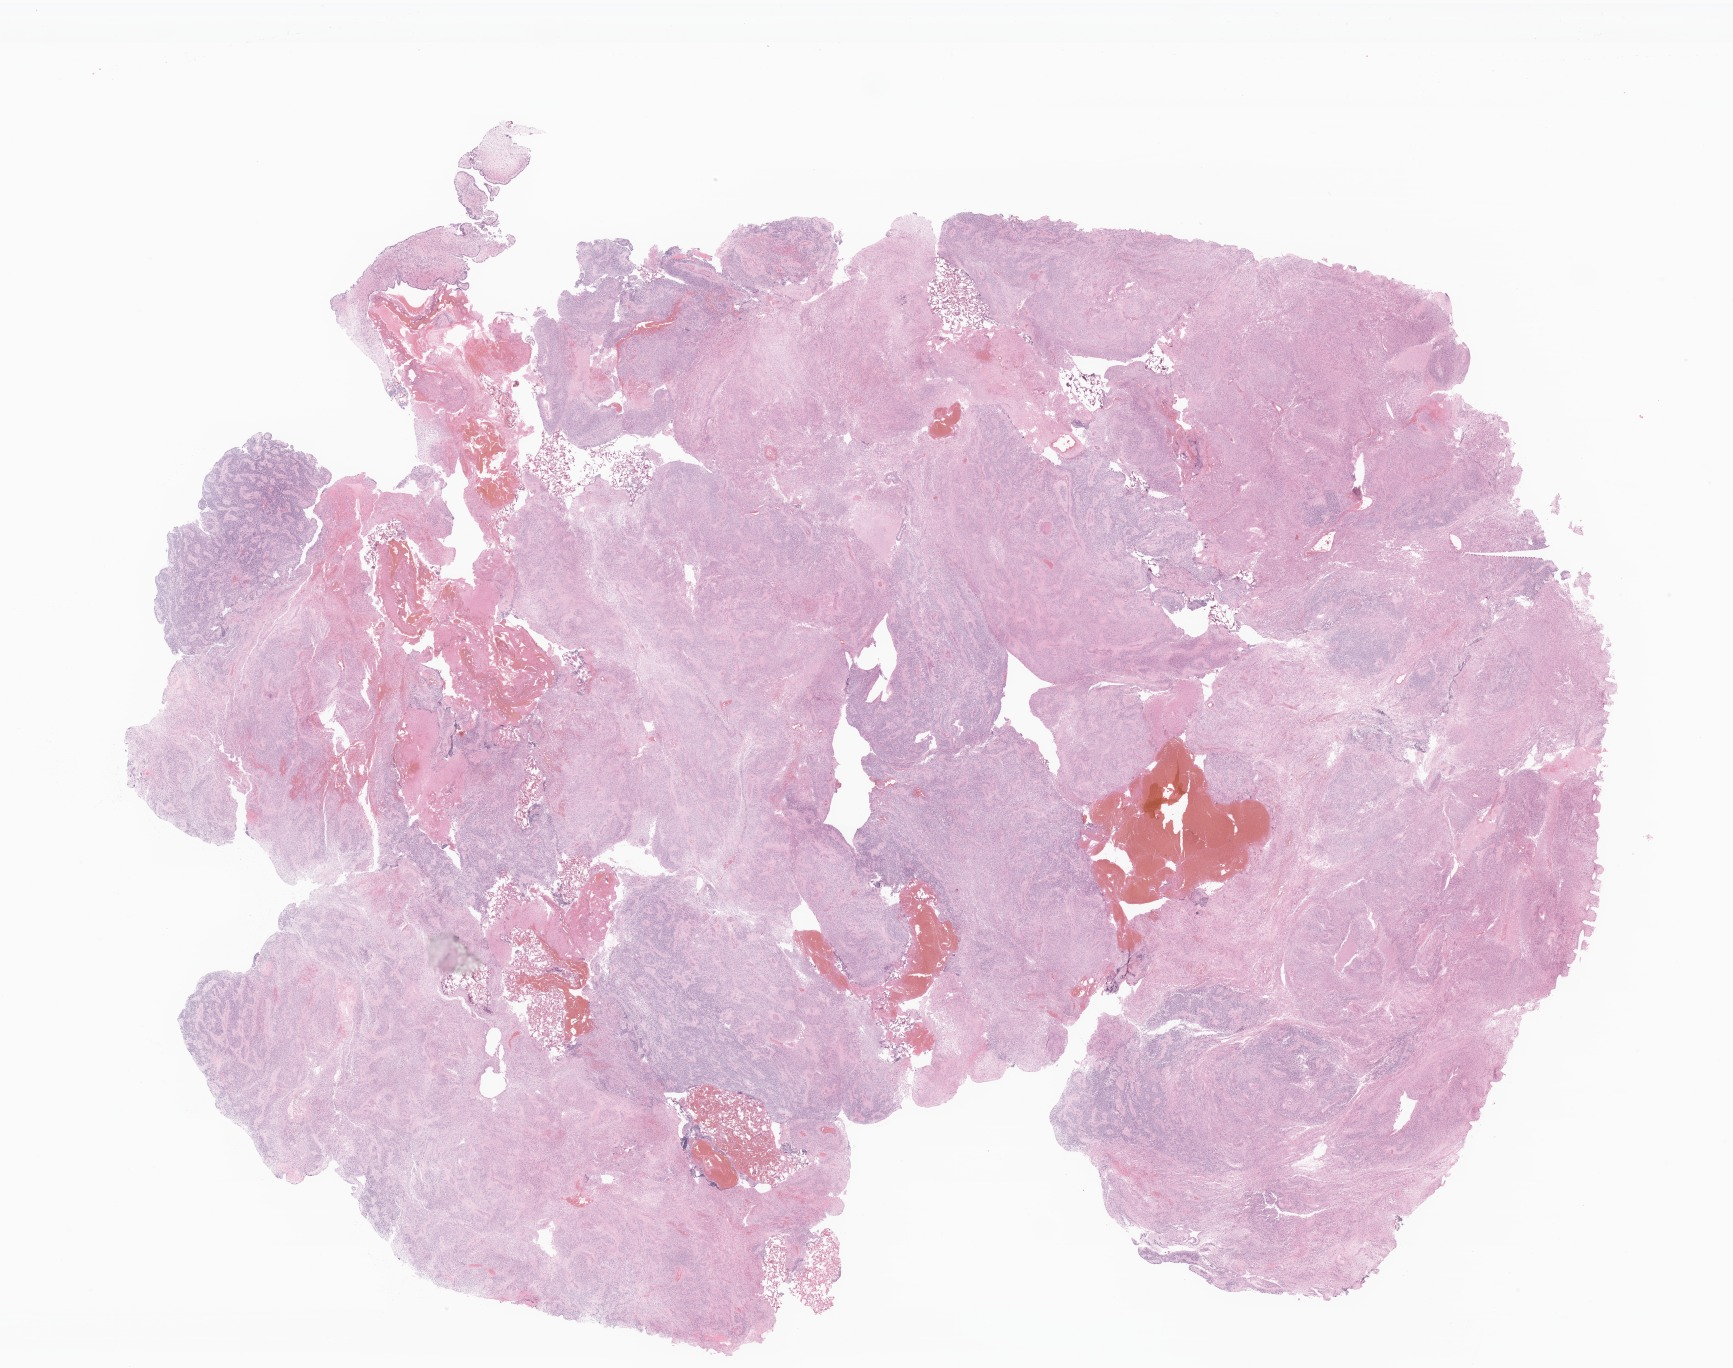
Haematoxylin and eosin whole-slide image of tumor tissue from the brain, whole scanned area (about 29.2 x 23.1 mm) shown as a low-resolution overview. Formalin-fixed, paraffin-embedded (FFPE) tissue. Patient male; age 100 months (8 years 4 months).
* recorded diagnosis: Ependymoma, NOS